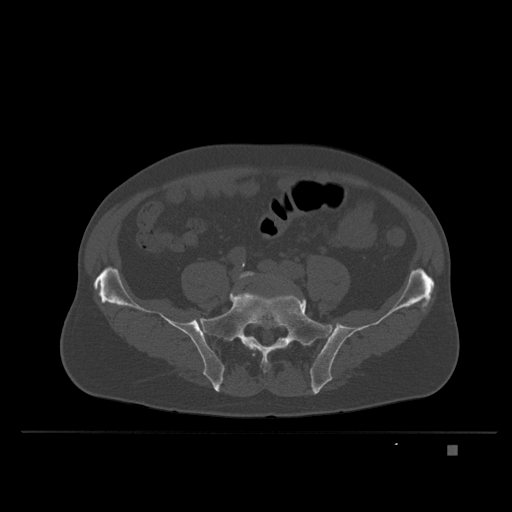
CT including the spine, one axial slice. Slice 42 of 435 in the series (ordered by position). Bone window (W 1800 / L 400 HU). 1.5 mm slice thickness. 512 × 512 image matrix, field of view 434 × 434 mm. Patient: male, 73 years. From the clinical record (not read from this slice): primary cancer: skin.
Outlined on this slice (semi-automatically segmented with operator editing):
- L5 vertebra: box from (x=238, y=271) to (x=291, y=357) px